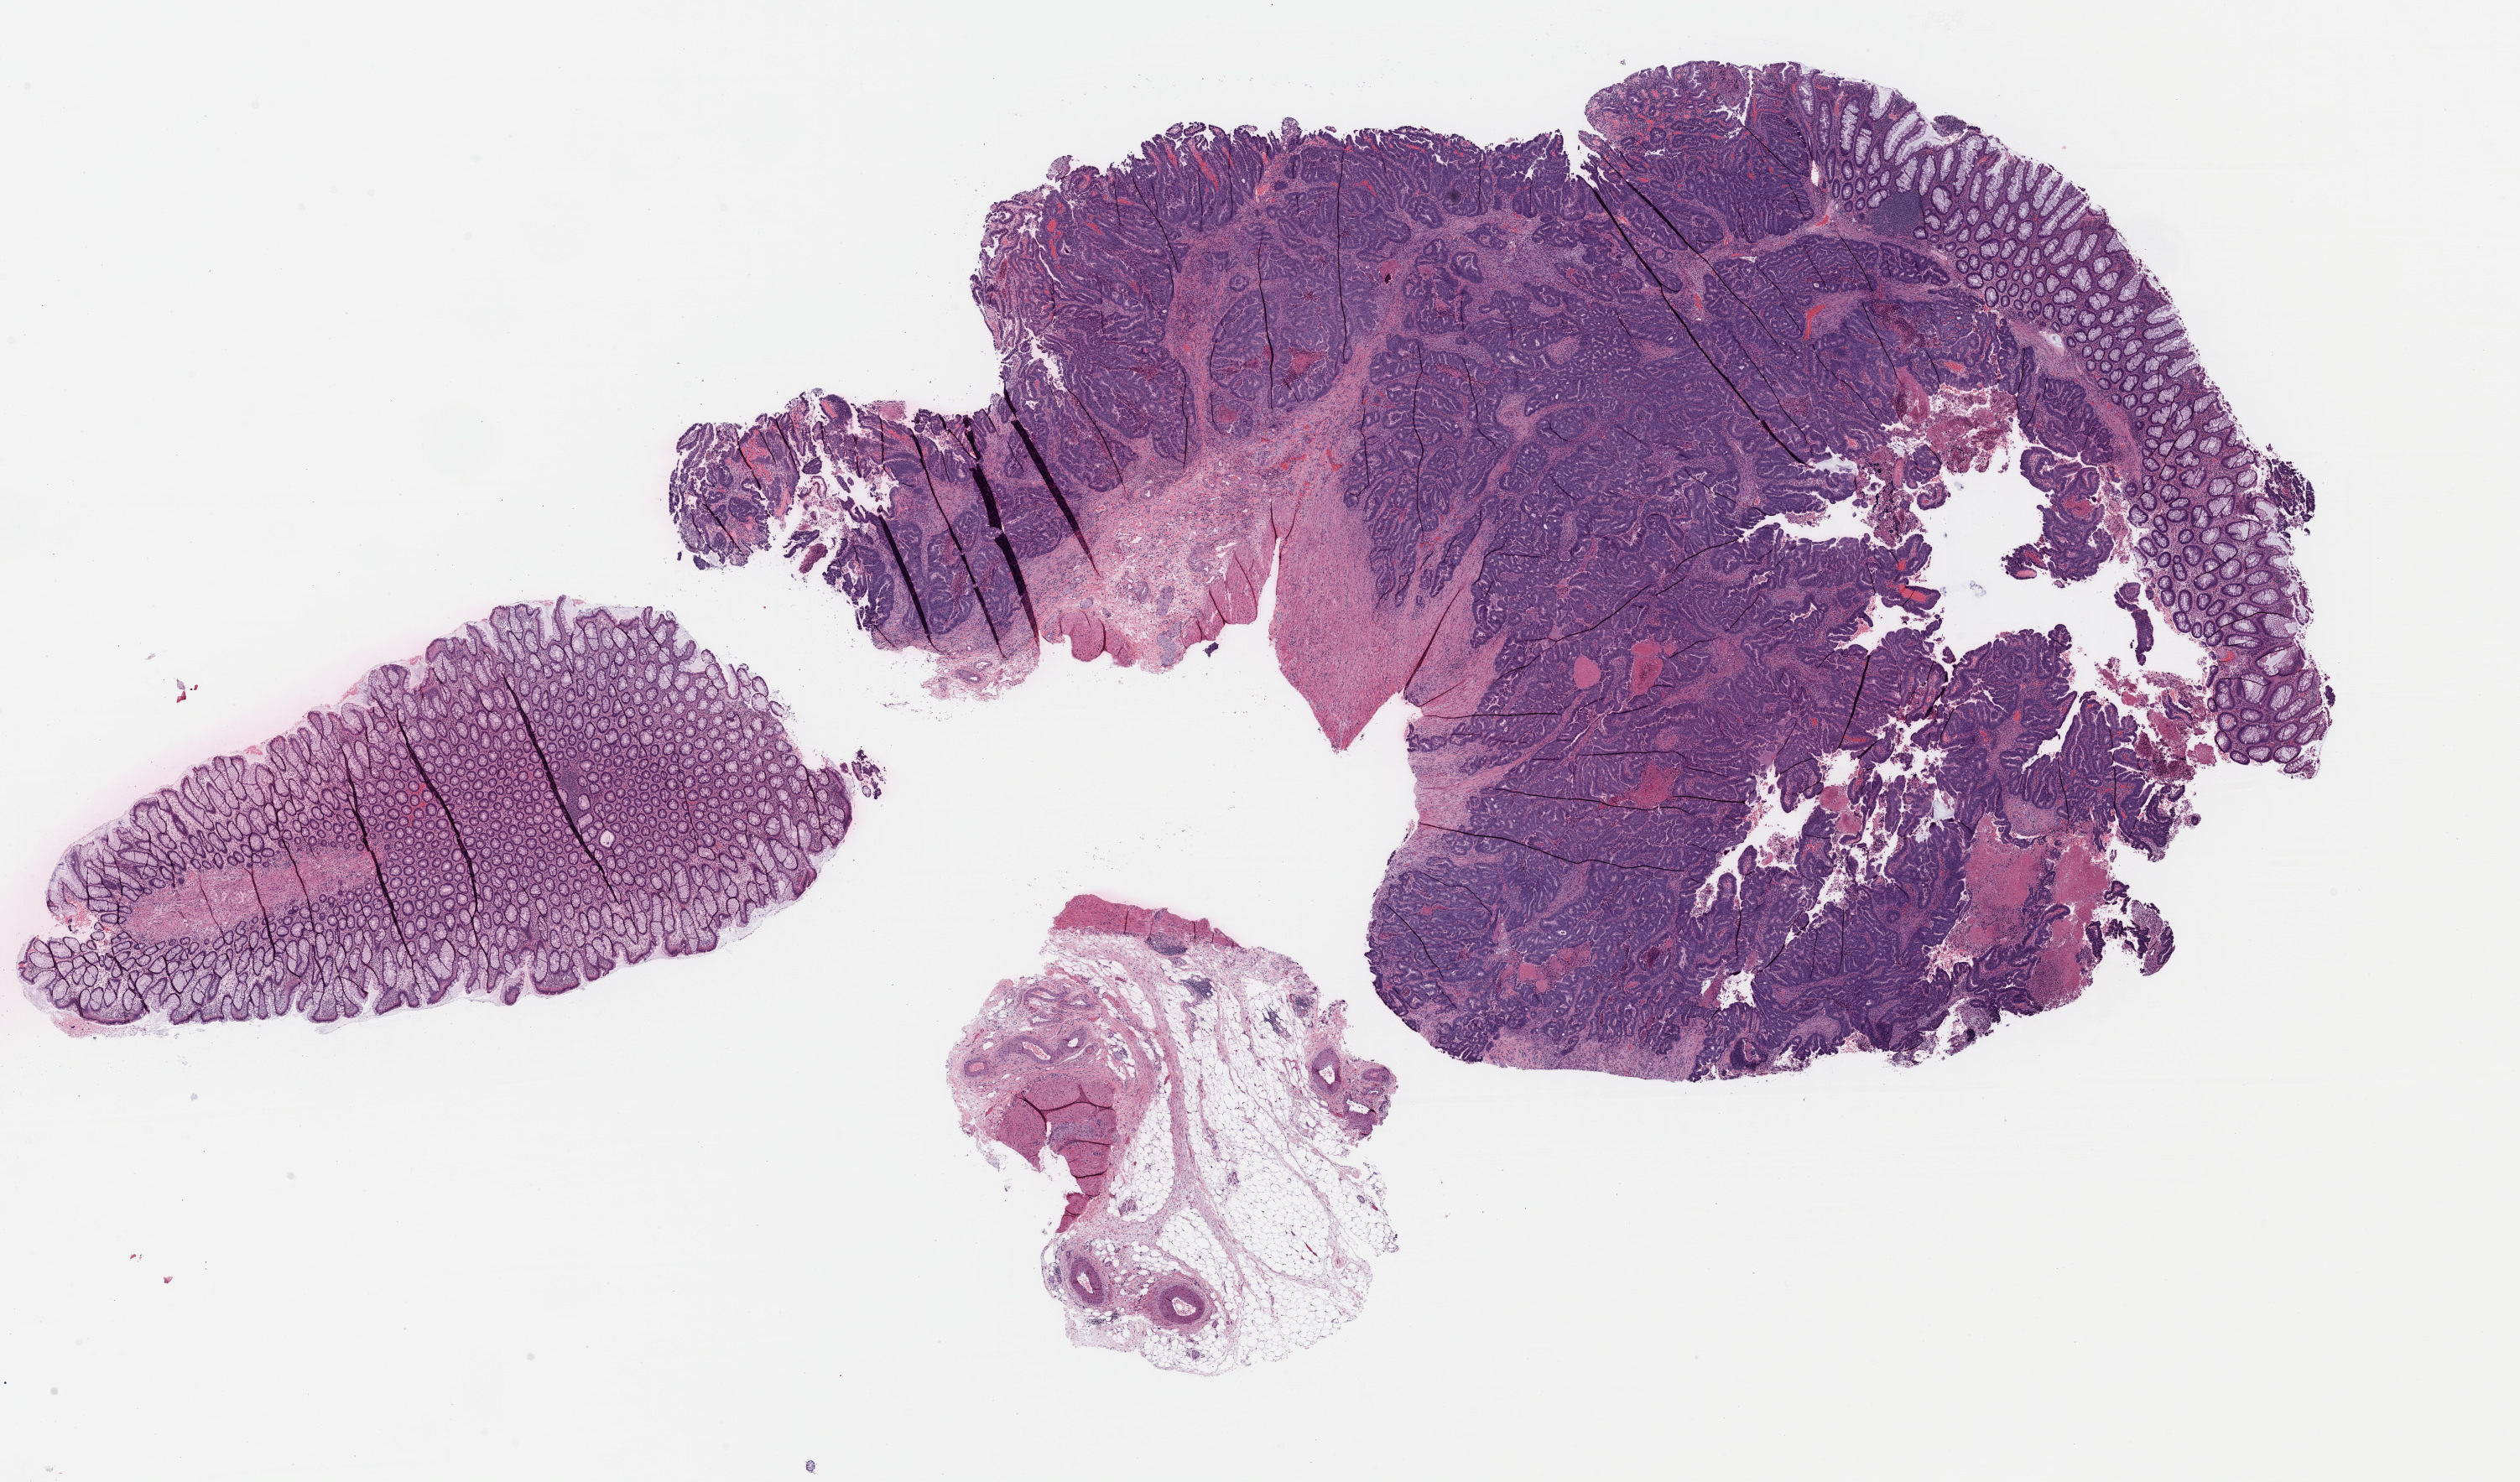
Digitized Hematoxylin and eosin (H&E) stained tissue section (whole slide) — low-resolution overview of the scanned area, about 23.7 x 13.9 mm. Formalin-fixed paraffin-embedded (FFPE) diagnostic section. Primary tumour sample from the colon. Patient: male, age at initial diagnosis 57 years.
Lymph nodes positive (case pathology): 3 of 25 examined. Pathologic diagnosis: Adenocarcinoma, NOS (sigmoid colon). AJCC pathologic stage: IIIB (6th edition).